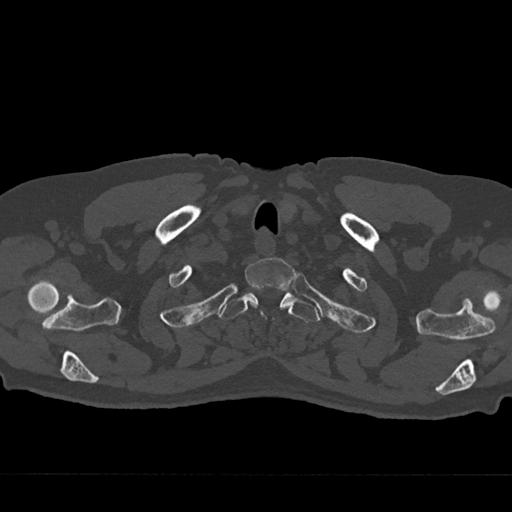
CT including the spine, one axial slice; slice 633 of 797 in the series (ordered by position); reconstruction kernel Br40s/3; bone window (W 1800 / L 400 HU); 0.5 mm slice thickness; 512 × 512 image matrix, field of view 377 × 377 mm. Patient: male, 75 years. From the clinical record (not read from this slice): primary cancer: renal; vertebrae with lytic lesions (as recorded): T4.
Outlined on this slice (semi-automatic segmentation, software-assisted and operator-edited):
- T1 vertebra: bounding box [x1, y1, x2, y2] px = [245, 258, 295, 315]
- T2 vertebra: [220, 289, 320, 323]